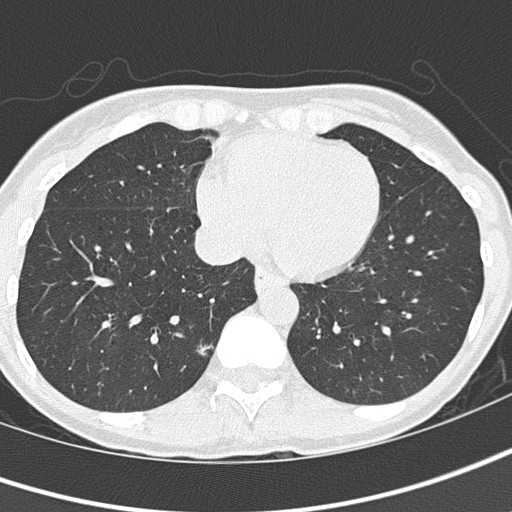
Low-dose screening chest CT, axial slice. First (baseline) screen. Lung window (W 1500 / L -600 HU). 2 mm slice thickness. Lung (sharp) reconstruction kernel (B50f). Female participant, aged 57 years at enrolment. Current smoker at enrolment.
Expert reader's lesion annotation, bounding box <179,337,219,367> (left, top, right, bottom; pixels). The exam's reader record, not a measurement of the box and not confirmed to be the same lesion: non-calcified nodule or mass ≥4 mm, right lower lobe, 11 × 6 mm, mixed attenuation. Official screen result: positive, change unspecified: nodule(s) >= 4 mm or enlarging nodule(s), mass(es), or other non-specific abnormalities suspicious for lung cancer. Later outcome: lung cancer diagnosed 61 days after this screen — adenocarcinoma, NOS, right lower lobe, moderately differentiated (G2), stage IA (AJCC 6th edition), 8 mm at pathology.